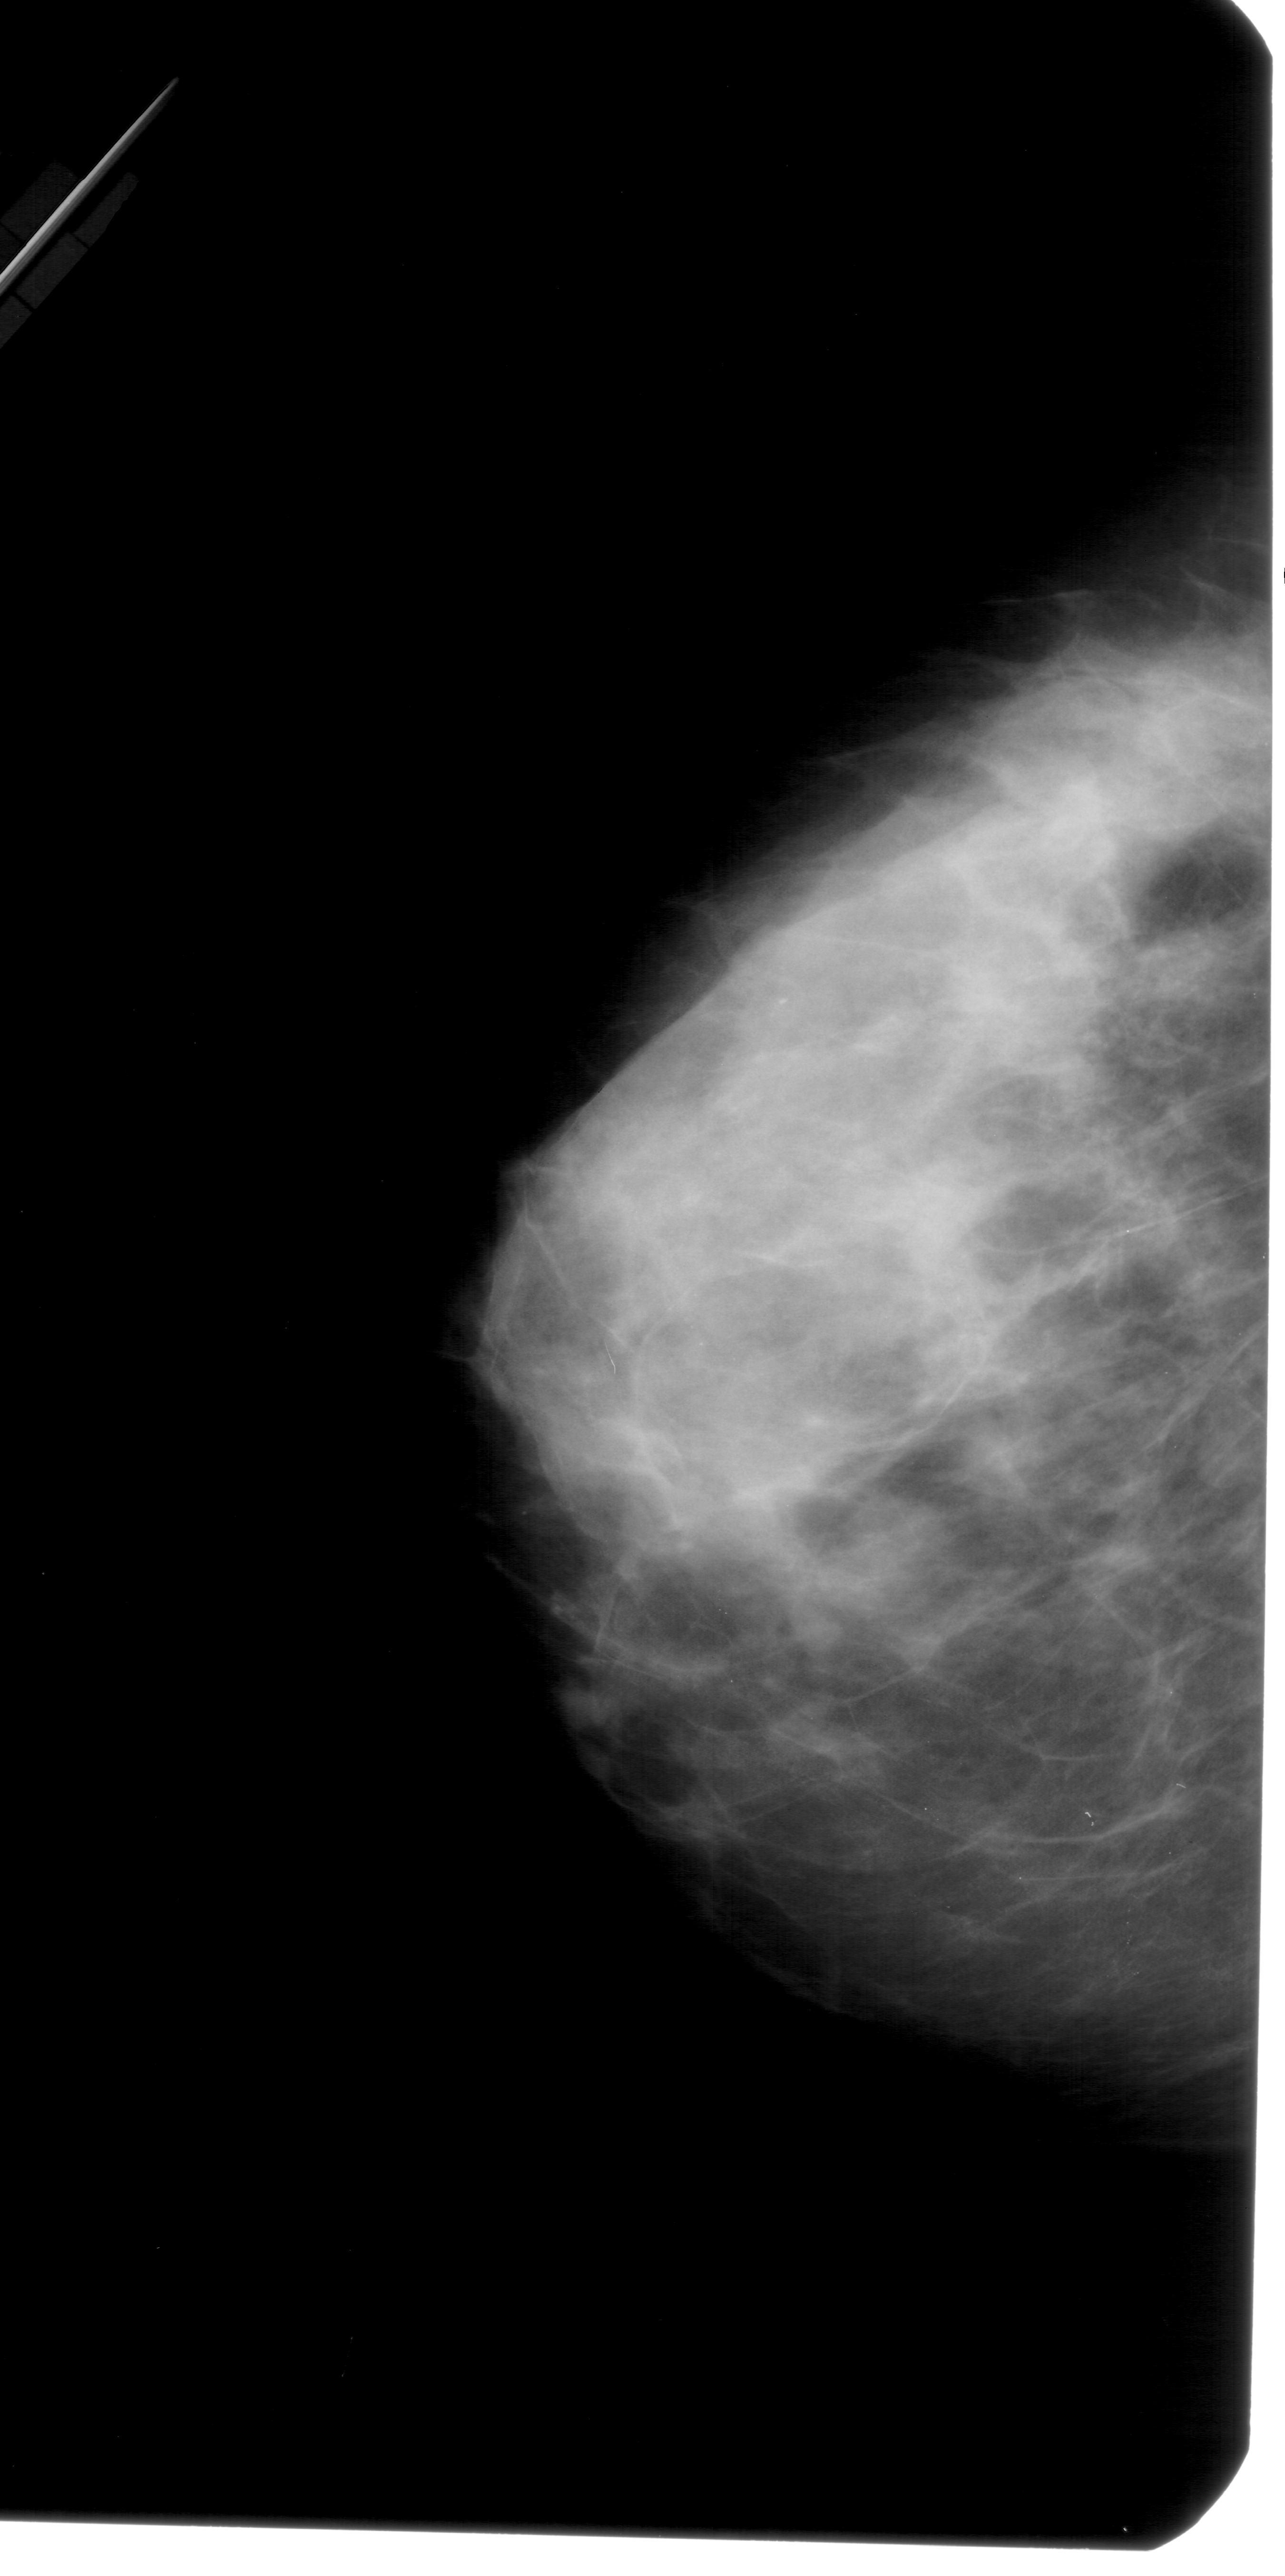
Digitized screen-film mammogram, left breast, craniocaudal (CC) view.
Marked abnormality: calcifications, morphology punctate, distribution regional; BI-RADS assessment category 4; subtlety rating 1 on a 1 (subtle) to 5 (obvious) scale; pathology result (as recorded, not read from the image): malignant.